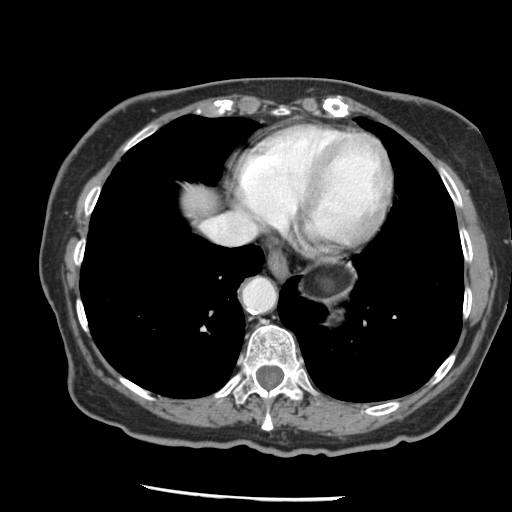
Contrast-enhanced abdominal CT, one axial slice. Slice 122 of 148 in the series (ordered by position). Reconstruction kernel STANDARD. 120 kVp. Soft-tissue window (W 400 / L 40 HU). 2.5 mm slice thickness. 512 × 512 image matrix, field of view 330 × 330 mm. Female patient, age 85 years. From the clinical record (not read from this slice): diagnosis: colorectal cancer liver metastases, imaged before liver resection; multiple liver metastases: no; largest metastasis: 0.9 cm; chemotherapy before resection: yes.
Outlined on this slice (outlined manually by an expert reader):
- hepatic veins: box from (x=202, y=216) to (x=235, y=242) px
- liver: (x=179, y=186)–(x=216, y=216)
- planned liver remnant (the part of the liver to remain after resection): (x=179, y=186)–(x=216, y=216)